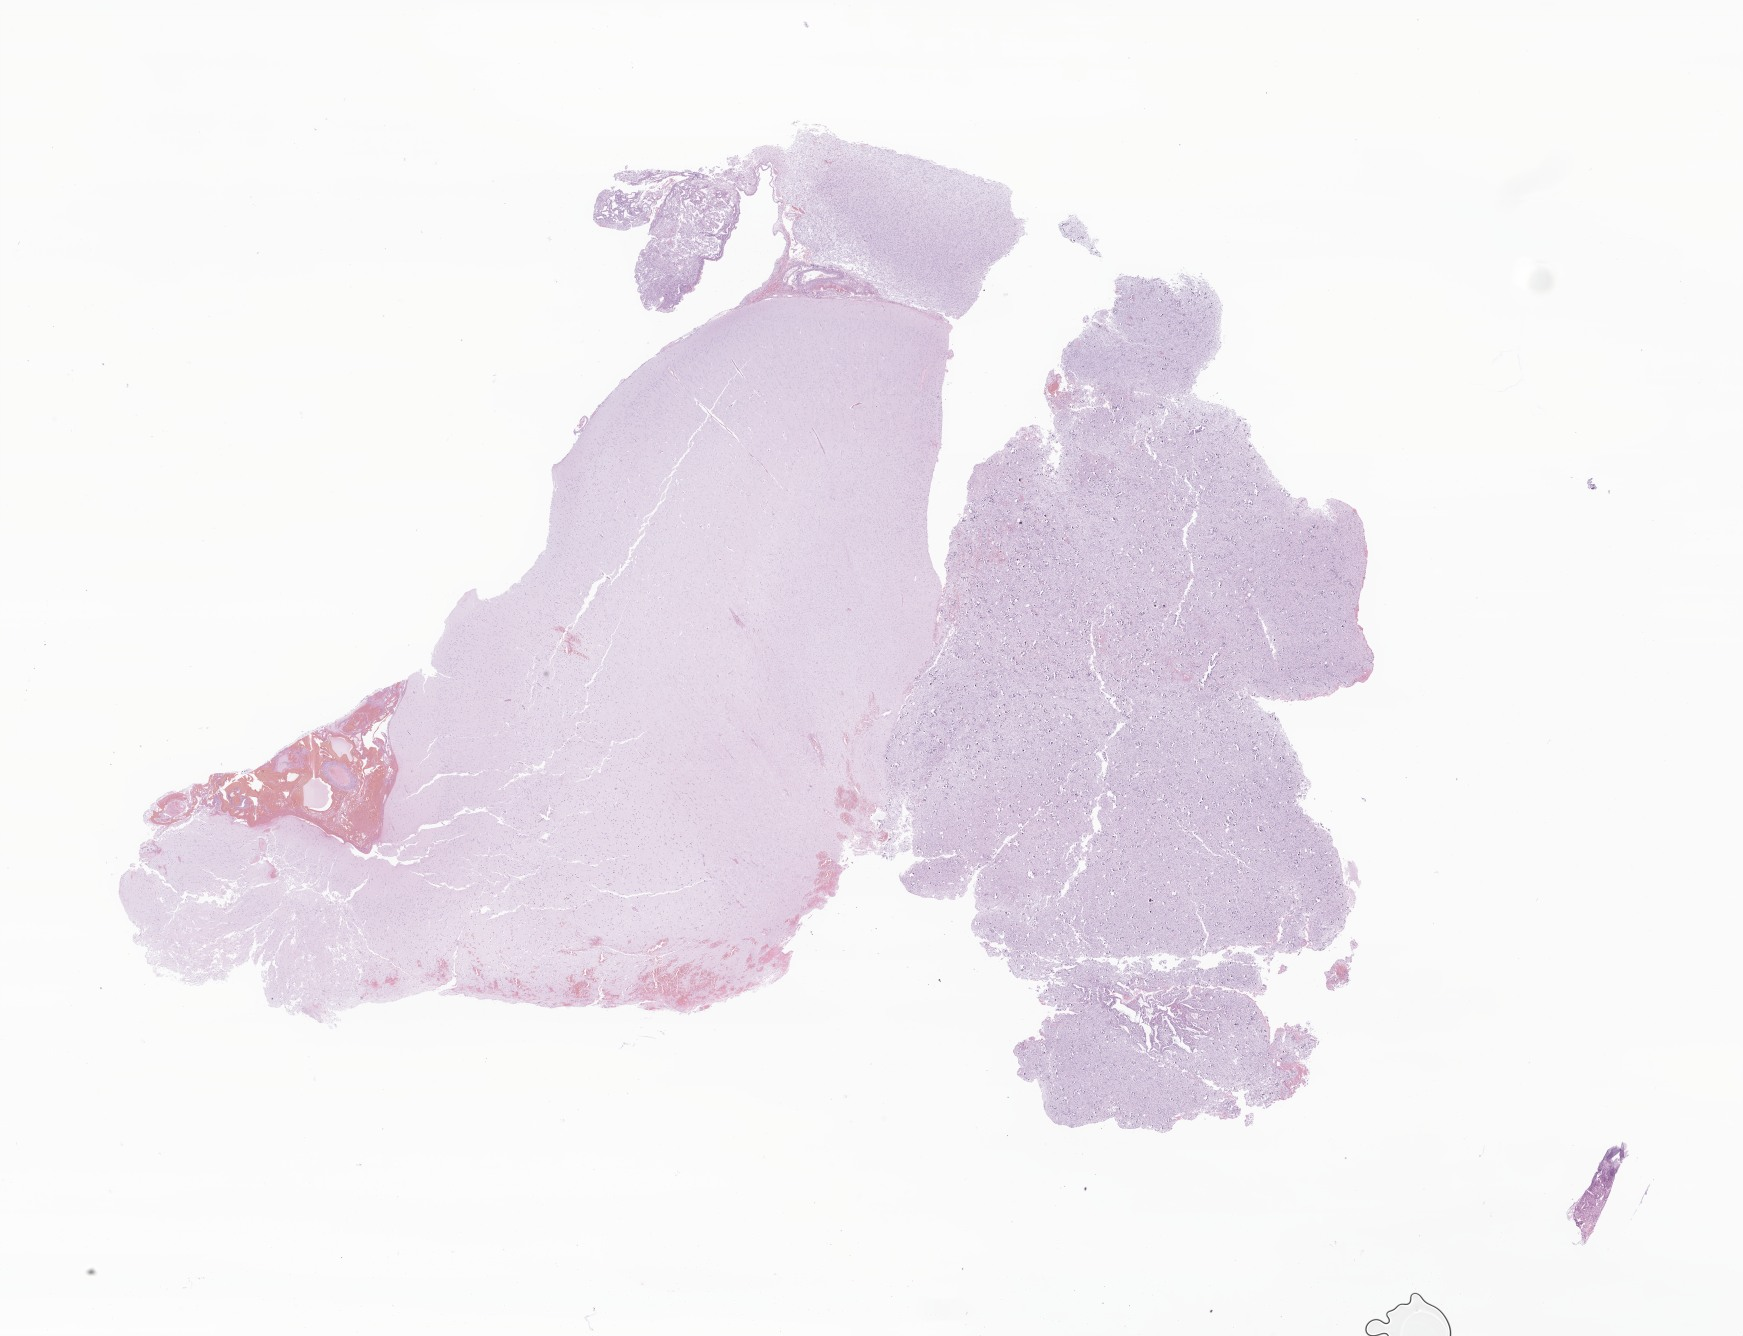
Whole-slide image, haematoxylin and eosin stain of tumor tissue from the frontal lobe, whole scanned area (about 29.4 x 22.5 mm) shown as a low-resolution overview. FFPE section. Female patient, age 619 days (about 1.7 years).
• recorded diagnosis: Ganglioglioma, NOS